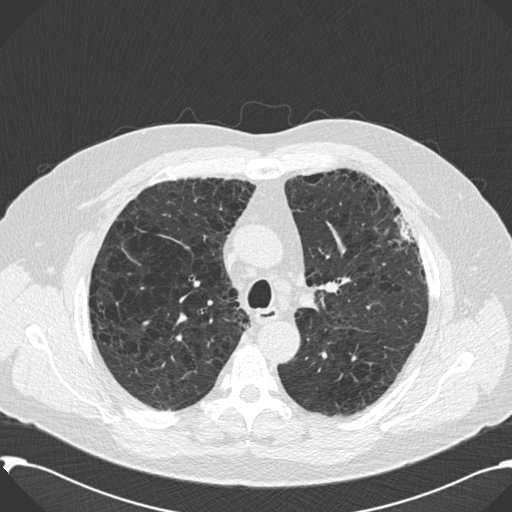
Chest CT (low-dose screening protocol), one axial image. Second screening round (one year after baseline). Lung window (W 1500 / L -600 HU). 120 kVp. Slice 54 of 199 in the series. 512 × 512 image matrix. Male participant, aged 59 years at enrolment. Current smoker at enrolment.
Lesion marked by an expert reader, bounding box [x1, y1, x2, y2] px = [361, 191, 427, 291]. No non-calcified nodule or mass ≥4 mm was recorded by the screening reader at this exam. Official screen result: negative screen, significant abnormalities not suspicious for lung cancer. Later outcome: lung cancer diagnosed 518 days after this screen — bronchiolo-alveolar carcinoma, mixed mucinous and non-mucinous, left upper lobe, stage IA (AJCC 6th edition), 20 mm at pathology.